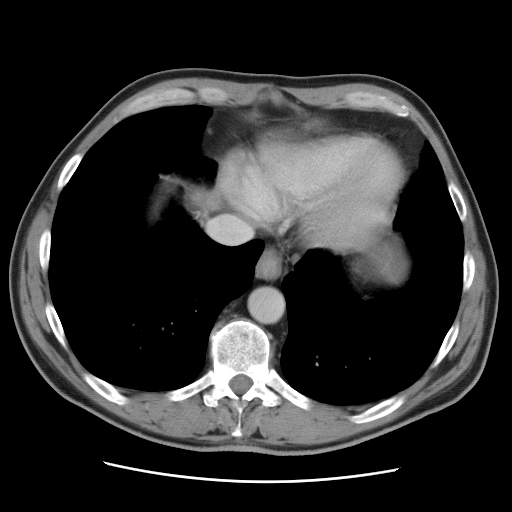
Contrast-enhanced abdominal CT, one axial slice; position 83 of 89 along the scan axis; 120 kVp; soft-tissue window (W 400 / L 40 HU); 512 × 512 image matrix, field of view 366 × 366 mm. Male patient, age 59 years. From the clinical record (not read from this slice): diagnosis: colorectal cancer liver metastases, imaged before liver resection; multiple liver metastases: yes; largest metastasis: 0.6 cm.
Structures marked on this image (expert manual segmentation):
- liver: bounding box (x1, y1, x2, y2) in pixels: (147, 173, 229, 222)
- planned liver remnant (the part of the liver to remain after resection): (184, 172, 228, 214)